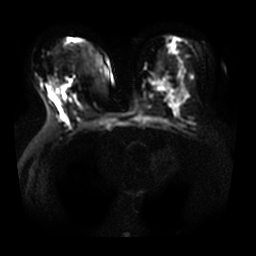
Breast MRI, one axial slice. Slice 15 of 33 in the series (ordered by position). Diffusion-weighted series; image 2 of 4 stored at this slice position (different b-values; order by instance number). 3 T. 5 mm slice thickness. 256 × 256 image matrix. Female patient.
Annotated regions visible in this slice (outlined manually by an expert reader):
- tumour on diffusion-weighted imaging: bounding box <65,77,73,87> (left, top, right, bottom; pixels)